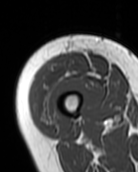
MRI of an extremity soft-tissue mass, one axial slice. Position 21 of 99 along the scan axis. MR volume resampled by the dataset authors to the PET/CT grid (not the native acquisition matrix). 3.27 mm slice thickness. 138 × 172 image matrix, field of view 135 × 168 mm. Female patient. Case-level facts recorded for this patient, not image findings: histological type: pleiomorphic undifferentiated sarcoma; grade: high; site of the primary tumour: right quadricep.
Annotated regions visible in this slice (expert contour drawn on MRI and transferred to this co-registered scan by the dataset authors):
- gross tumour volume including surrounding oedema: bounding box <32,52,88,122> (left, top, right, bottom; pixels)